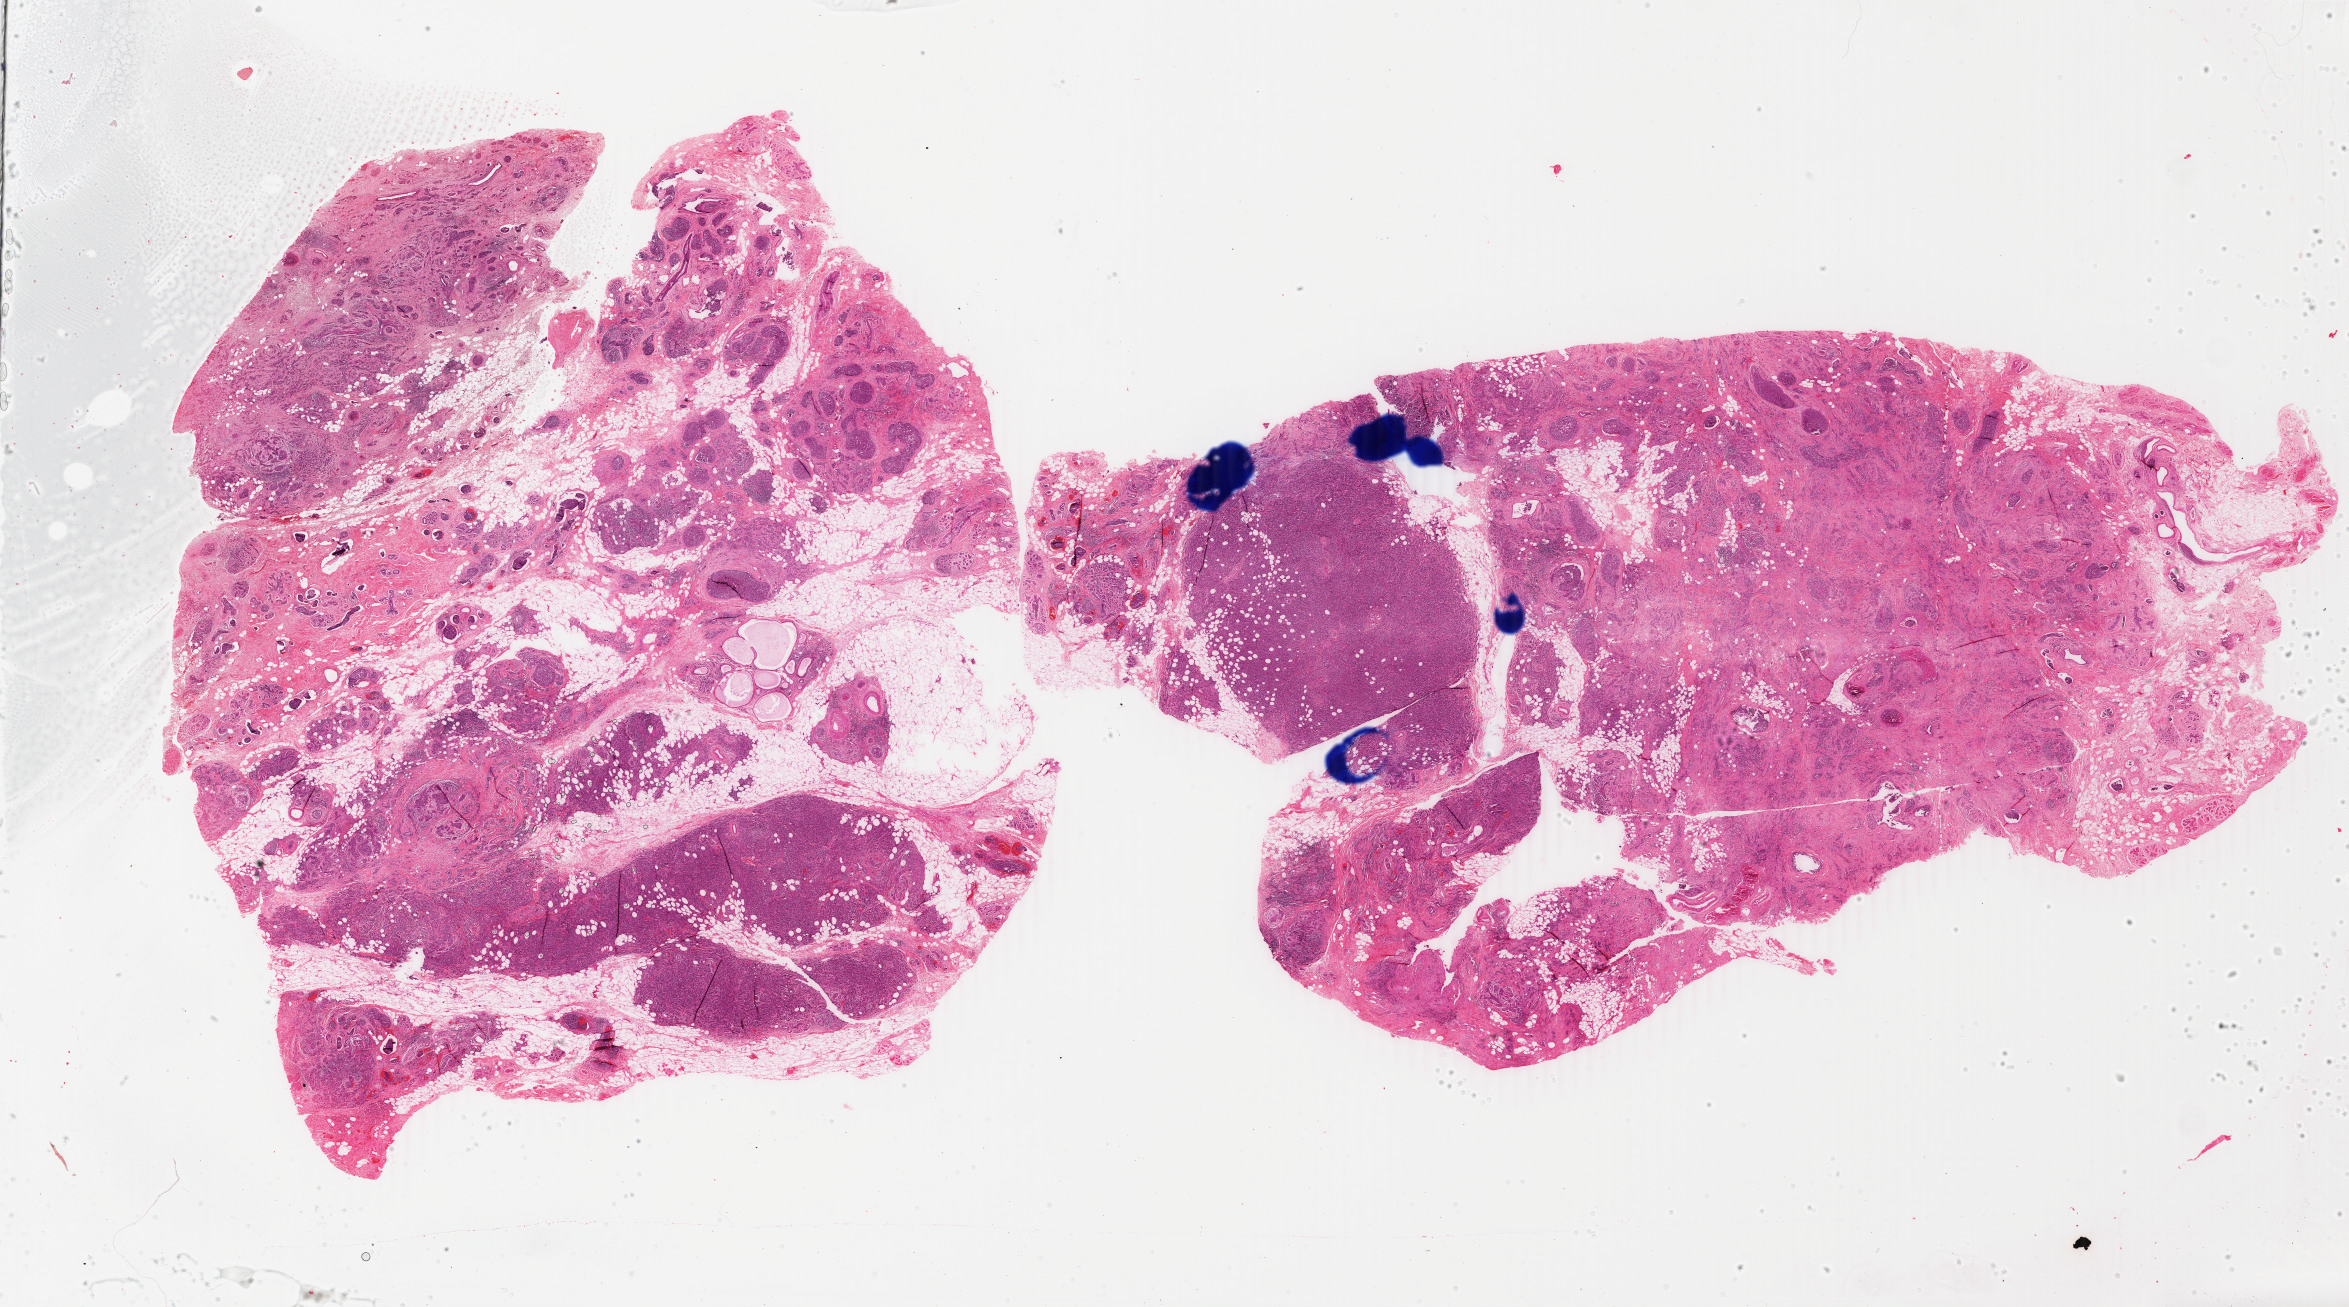
H&E-stained whole-slide image, whole scanned area (about 37.4 x 20.8 mm, acquisition: 40x scan) shown as a low-resolution overview, formalin-fixed paraffin-embedded (FFPE) diagnostic section, primary tumour sample from the breast. Female patient; age at initial diagnosis 49 years.
Laterality: left. Histologic diagnosis: Infiltrating duct carcinoma, NOS. AJCC pathologic stage: IIA (3rd edition).